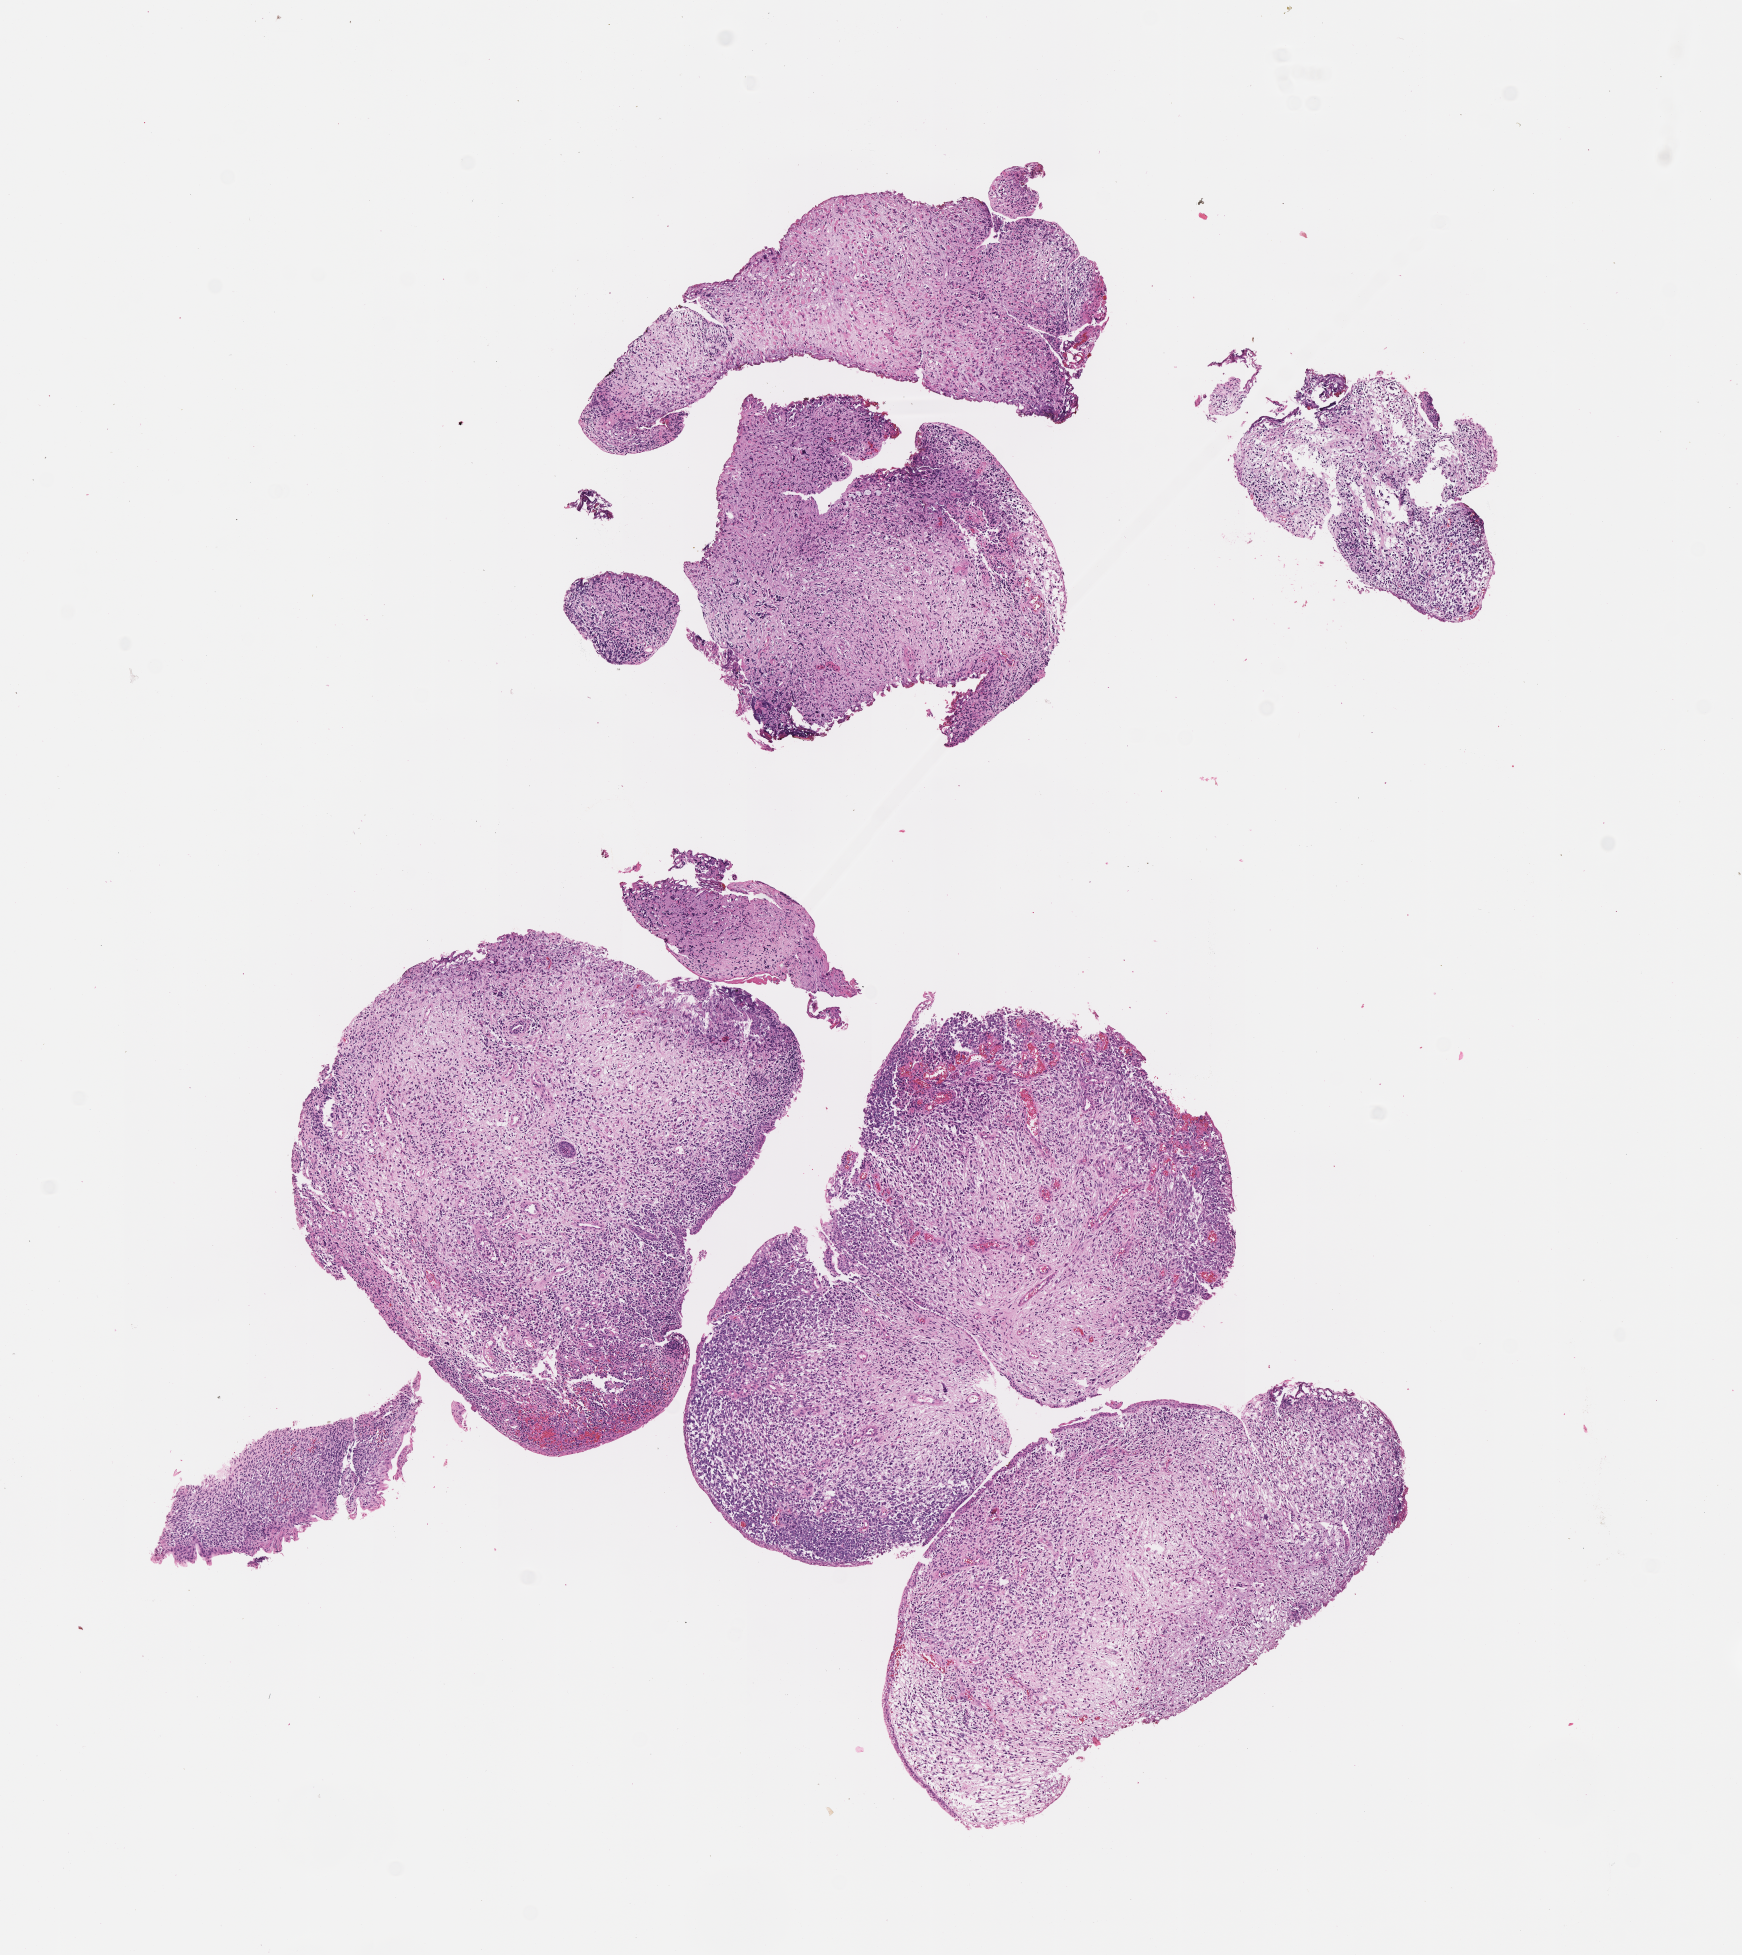
Whole-slide image, haematoxylin and eosin stain of tumor tissue, low-resolution overview of the scanned area, about 7.0 x 7.9 mm. Formalin-fixed paraffin-embedded section. Female patient, age at diagnosis 0.9 years.
Diagnosis: rhabdomyosarcoma; histological classification: botryoid.